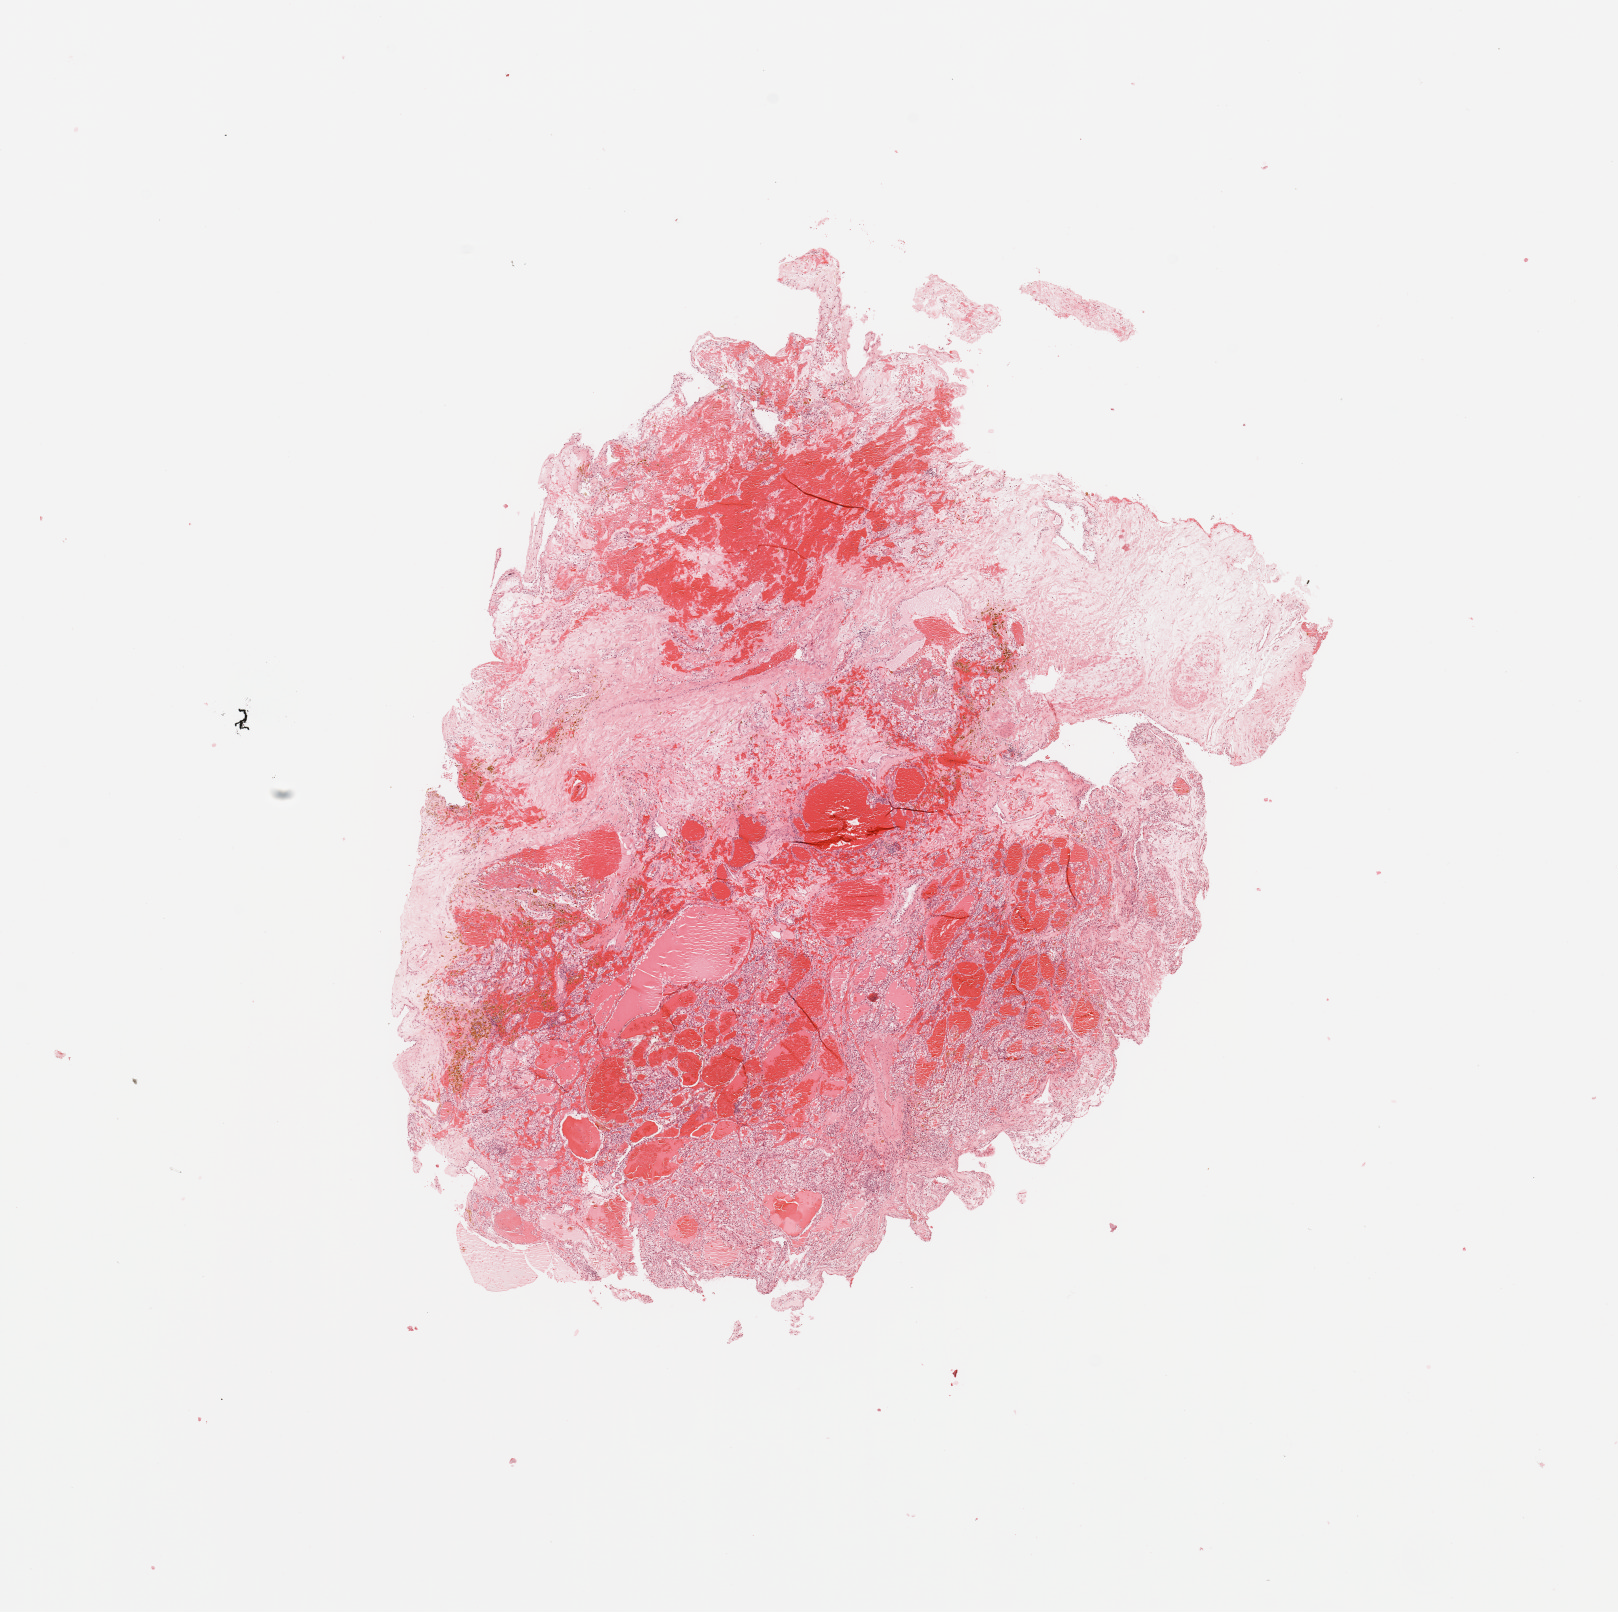
Digitized Hematoxylin and eosin (H&E) stained tissue section (whole slide), low-resolution overview of the scanned area, about 12.8 x 12.7 mm (slide scanned at 20x); tumour tissue sample, sampled site: kidney. Male, 67 y/o. Histologic grade: G2 (moderately differentiated). Slide review estimates, as recorded: tumour nuclei 80%, necrosis 5%.
• AJCC pathologic stage: I
• primary tumour site (as recorded): lower pole
• diagnosis: Renal cell carcinoma, NOS